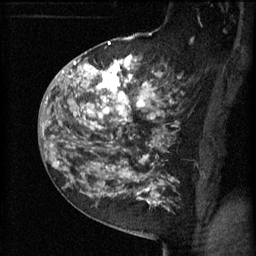
Breast MRI (dynamic contrast-enhanced), one sagittal slice; position 35 of 60 along the scan axis; 3 images stored at this slice position (order not interpretable as contrast timing); 1.5 T; TE 4.2 ms, TR 11 ms; 2 mm slice thickness; 256 × 256 image matrix, field of view 180 × 180 mm. Patient: female, 52 years.
Outlined on this slice (semi-automatically segmented with operator editing):
- analysis volume of interest (the breast-tissue region the enhancement analysis was run in; not a lesion): bounding box [x1, y1, x2, y2] px = [81, 52, 173, 157]
- tumour enhancement mask (voxels above the 70 % enhancement threshold inside the analysis volume of interest): [81, 54, 162, 157]